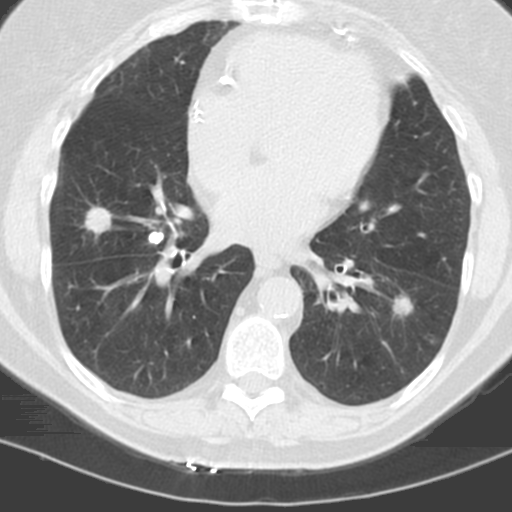
Low-dose screening chest CT, one axial slice. Slice 48 of 121 in the series (ordered by position). 120 kVp. Lung window (W 1500 / L -600 HU). 512 × 512 image matrix, field of view 278 × 278 mm.
Annotated regions visible in this slice (manually delineated by an expert):
- lesion 1 (tumor, lower lobe of left lung): bounding box (x1, y1, x2, y2) in pixels: (393, 296, 412, 316)
- lesion 3 (tumor, middle lobe of right lung): (85, 207, 111, 234)